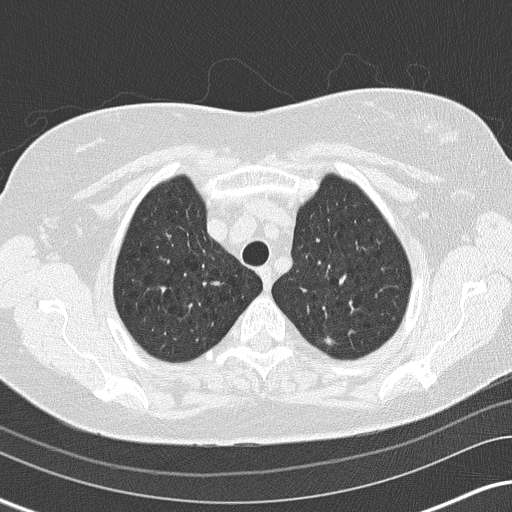
Low-dose screening chest CT, axial slice. First (baseline) screen. Lung window (W 1500 / L -600 HU). 2 mm slice thickness. Lung (sharp) reconstruction kernel (B50f). Slice 28 of 159 in the series. 512 × 512 image matrix. Female participant, aged 65 years at enrolment. Former smoker at enrolment.
- Expert-annotated lung lesion, bounding box (x1, y1, x2, y2) in pixels: (307, 322, 351, 359).
- The exam's reader record, not a measurement of the box and not confirmed to be the same lesion: non-calcified nodule or mass ≥4 mm, left upper lobe, 6 × 5 mm, soft tissue attenuation.
- Official screen result: positive, change unspecified: nodule(s) >= 4 mm or enlarging nodule(s), mass(es), or other non-specific abnormalities suspicious for lung cancer.
- Participant outcome: lung cancer diagnosed 800 days after this screen (after the third annual screen) — adenocarcinoma, NOS, left upper lobe, moderately differentiated (G2), stage IA (AJCC 6th edition), 8 mm at pathology.